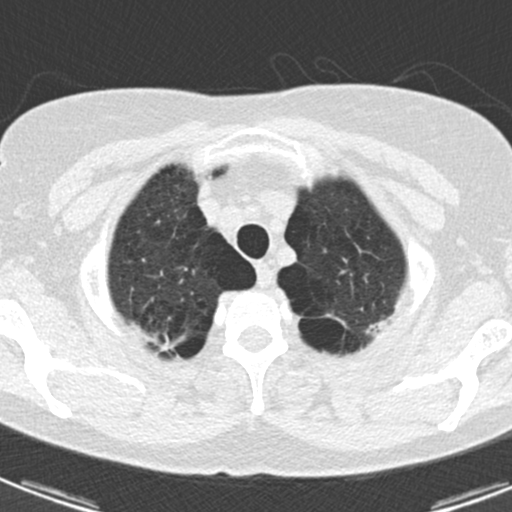
Low-dose screening chest CT, one axial slice; slice 156 of 174 in the series (ordered by position); 120 kVp; lung window (W 1500 / L -600 HU); 2 mm slice thickness; 512 × 512 image matrix.
Structures marked on this image (manually delineated by an expert):
- lesion 1 (tumor, upper lobe of right lung): box from (x=160, y=337) to (x=174, y=352) px